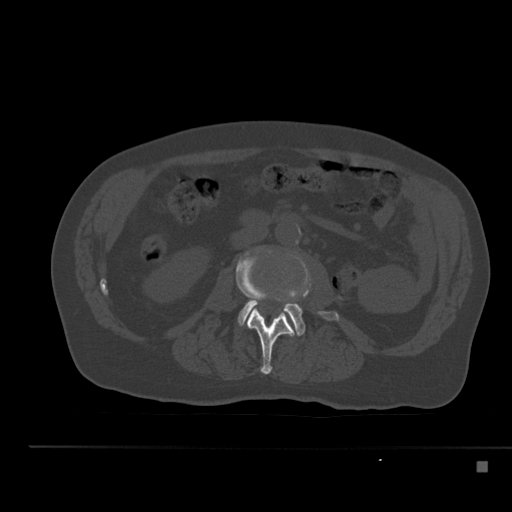
CT including the spine, one axial slice; slice 176 of 517 in the series (ordered by position); reconstruction kernel Br40s; bone window (W 1800 / L 400 HU); 512 × 512 image matrix, field of view 408 × 408 mm. Patient: male, 70 years. From the clinical record (not read from this slice): primary cancer: renal.
Annotated regions visible in this slice (semi-automatically segmented with operator editing):
- L2 vertebra: bounding box [x1, y1, x2, y2] px = [236, 253, 295, 374]
- L3 vertebra: [238, 280, 340, 336]